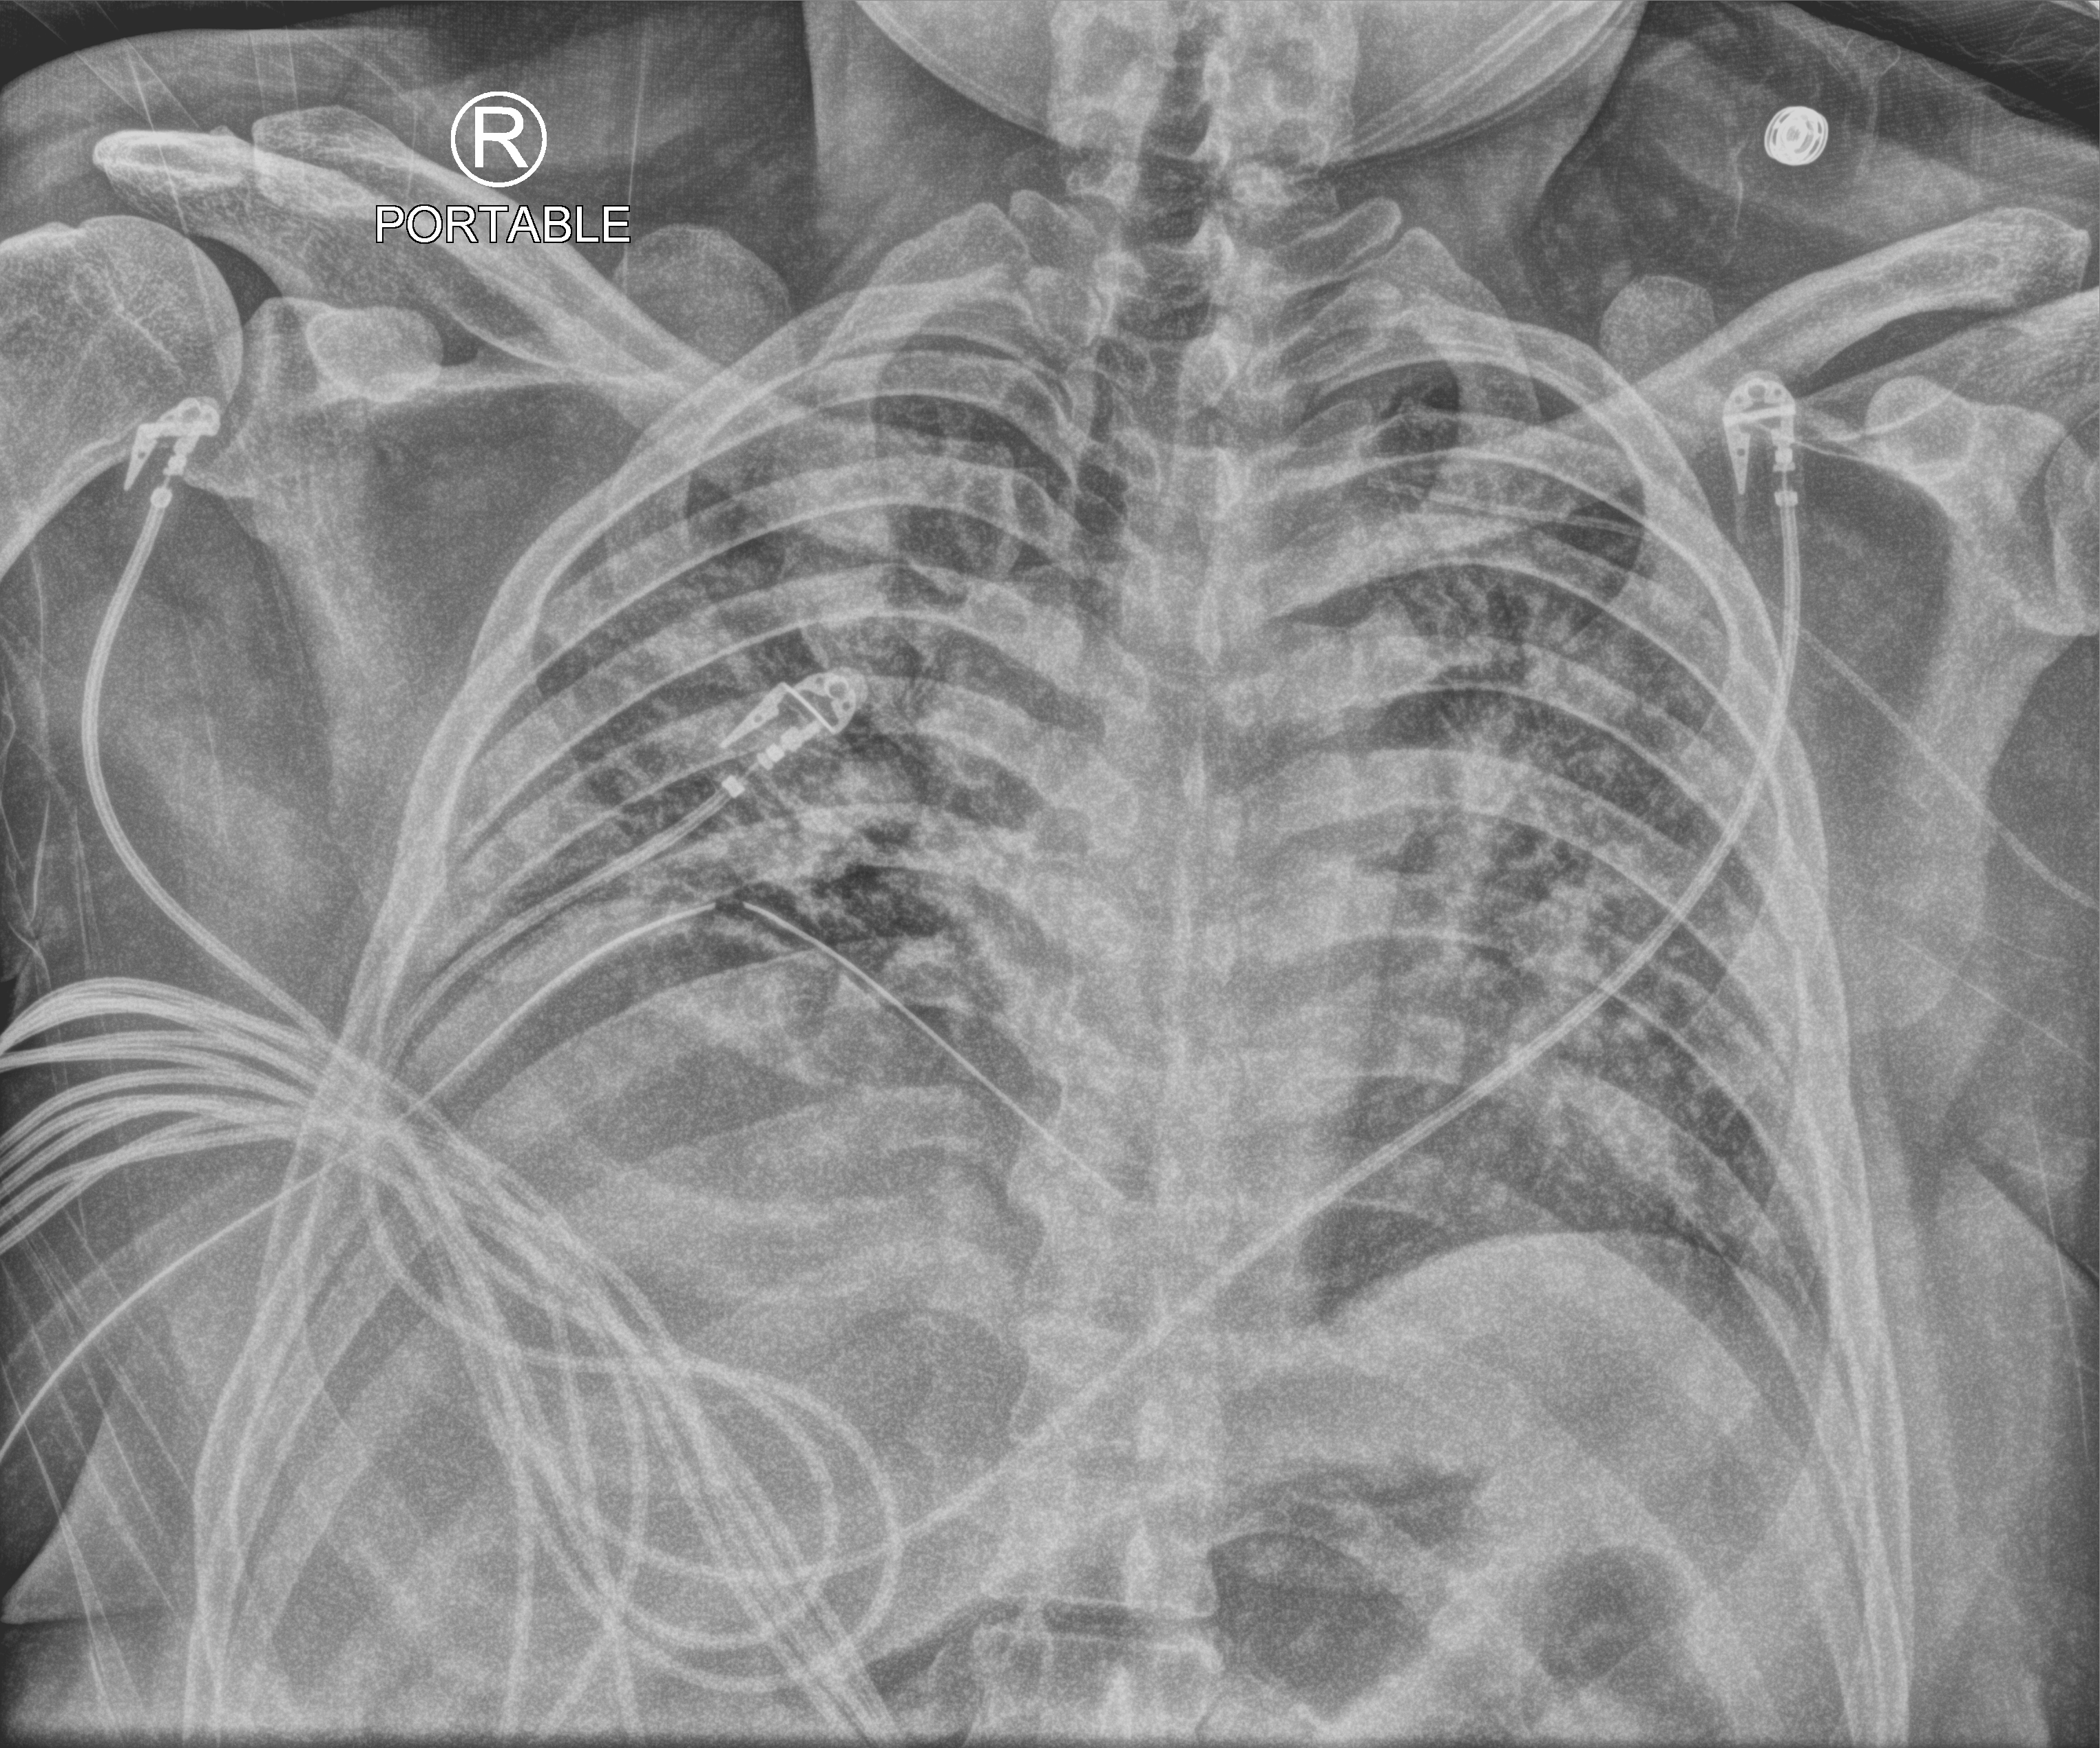
Portable chest radiograph, anteroposterior (AP) projection. Male patient hospitalised with COVID-19, age 18–59 years.
Admission-level facts for this patient (not findings on this image; timing relative to this image not recorded): mechanically ventilated during this hospital stay: yes; admitted to intensive care during this hospital stay: yes.